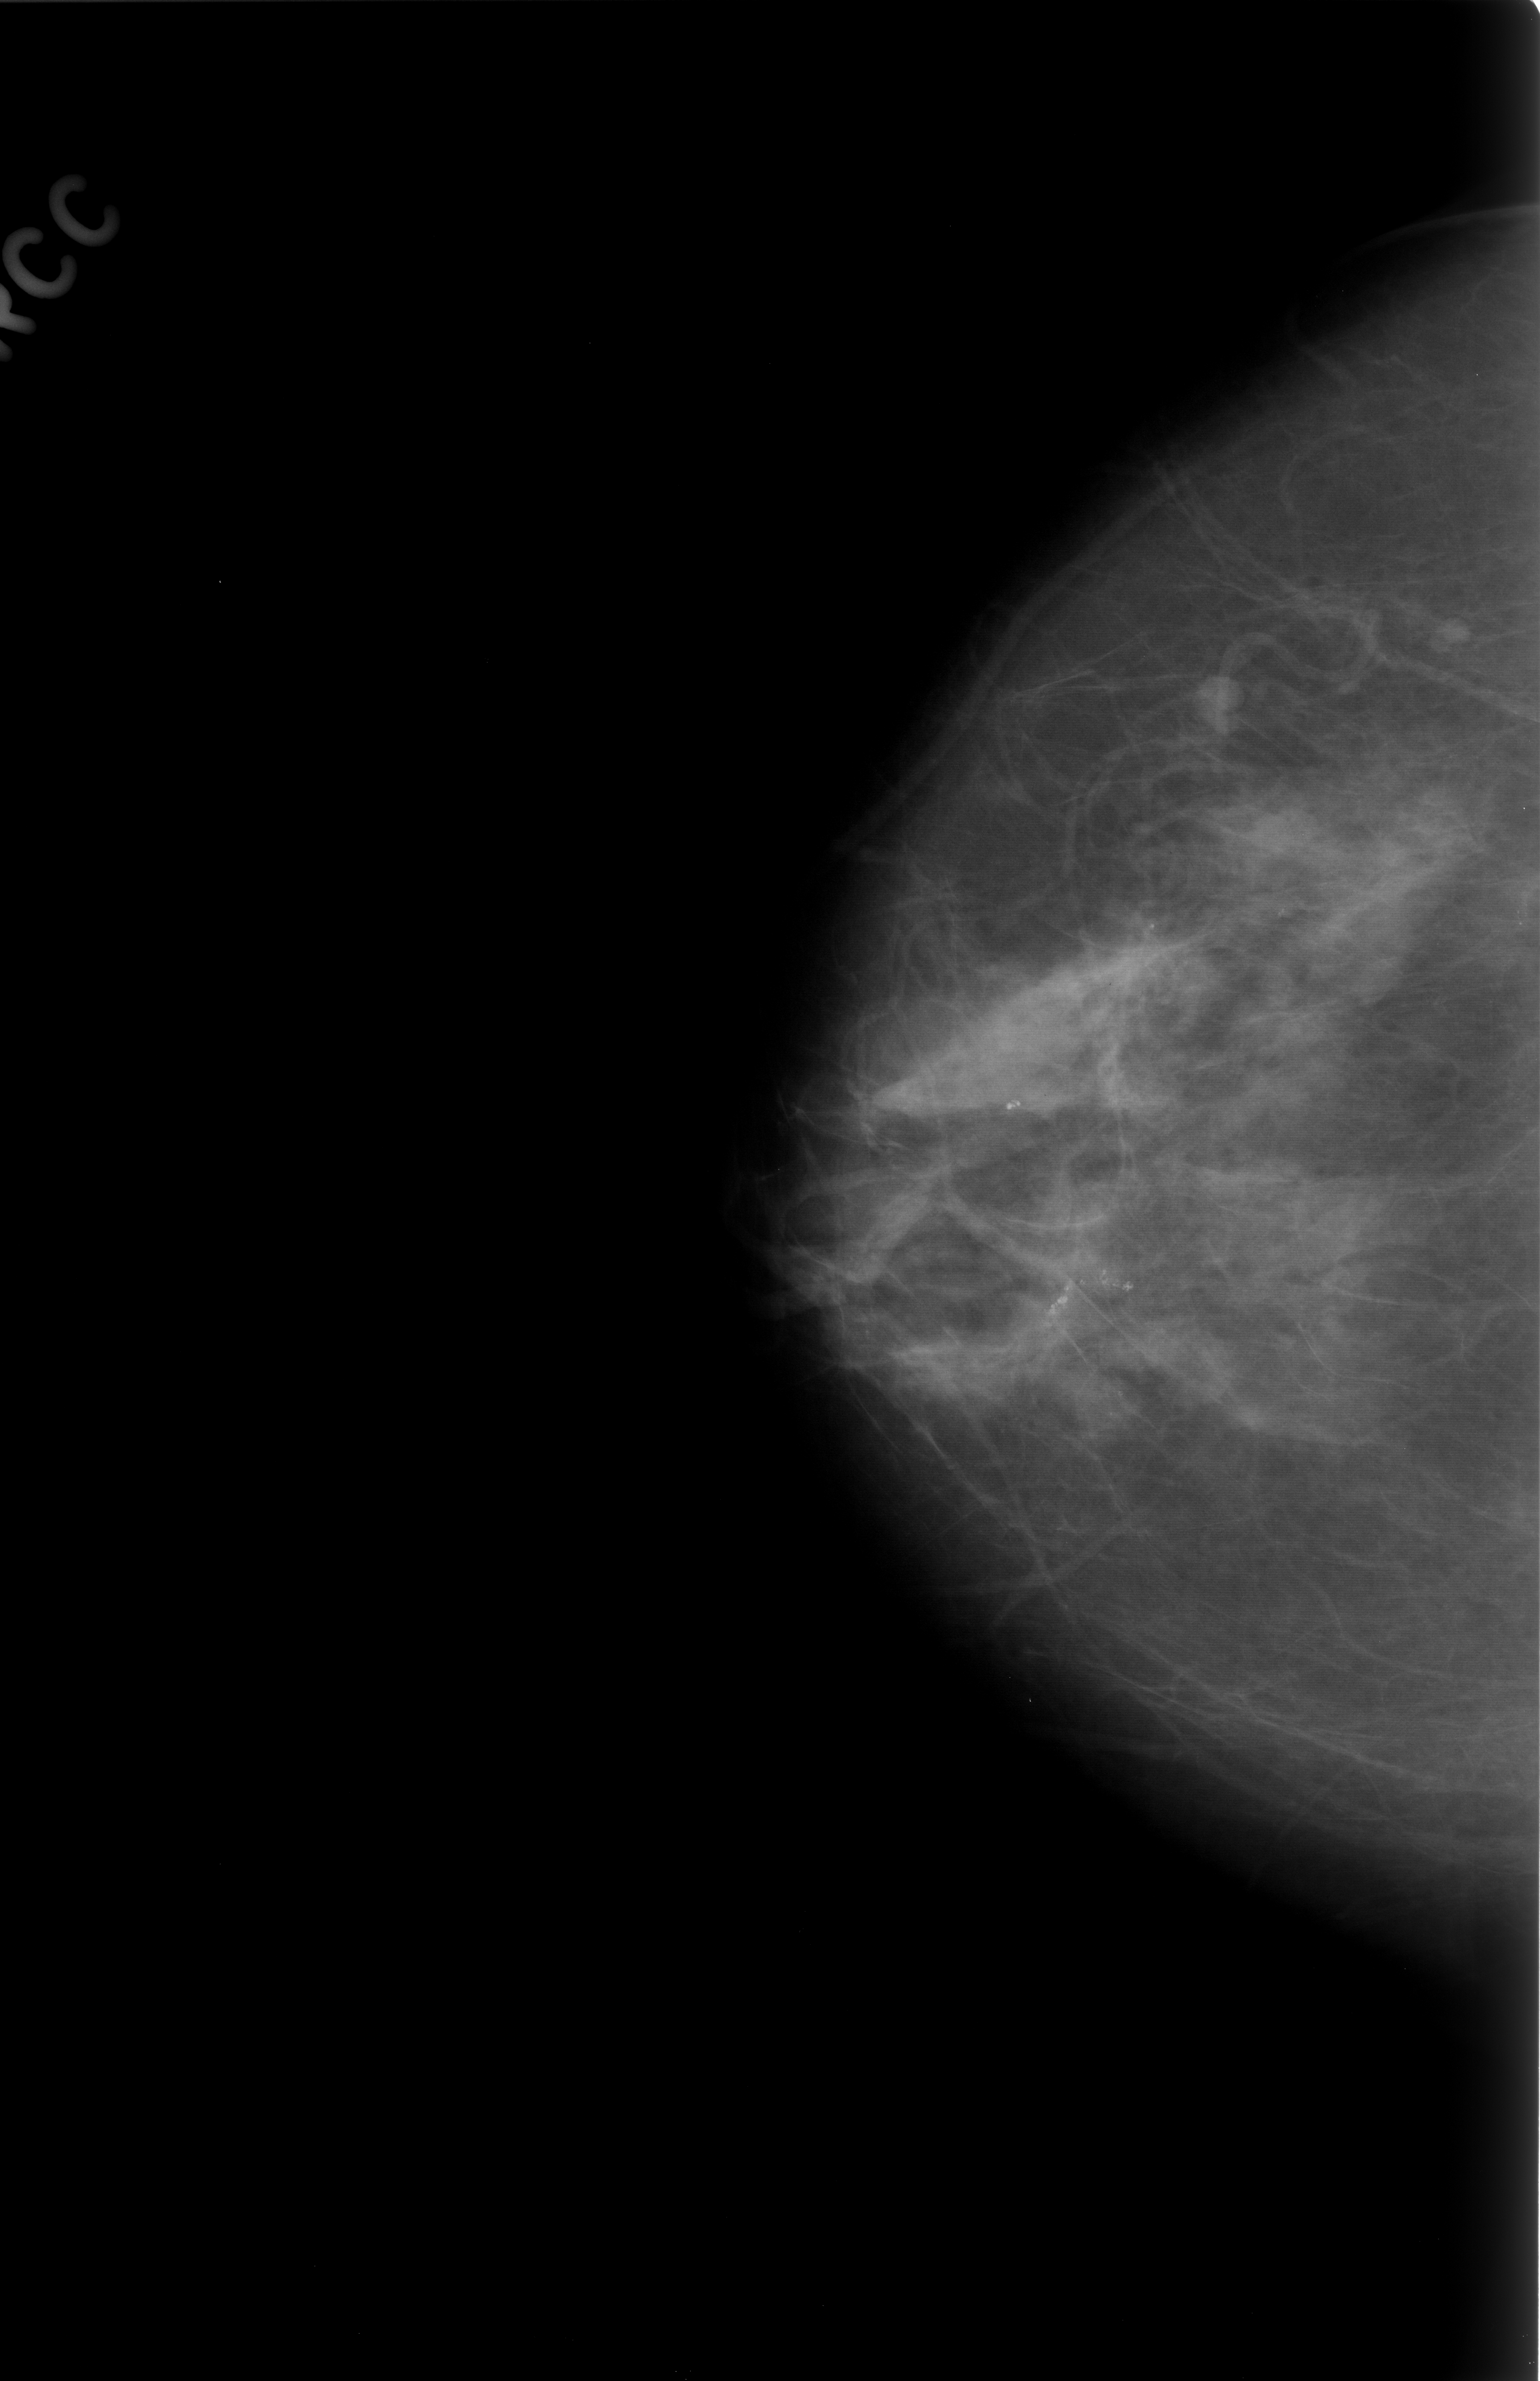
Scanned film-screen mammogram; right breast; CC view; BI-RADS breast density category 2 (scale 1–4); 1540 × 2381 image matrix.
Expert-marked regions of interest on this image (one box per marked abnormality):
- mass, shape lobulated, margins circumscribed; BI-RADS assessment category 2; outcome (as recorded, no biopsy): benign without callback (not worked up further): bounding box (x1, y1, x2, y2) in pixels: (1169, 647, 1257, 746)